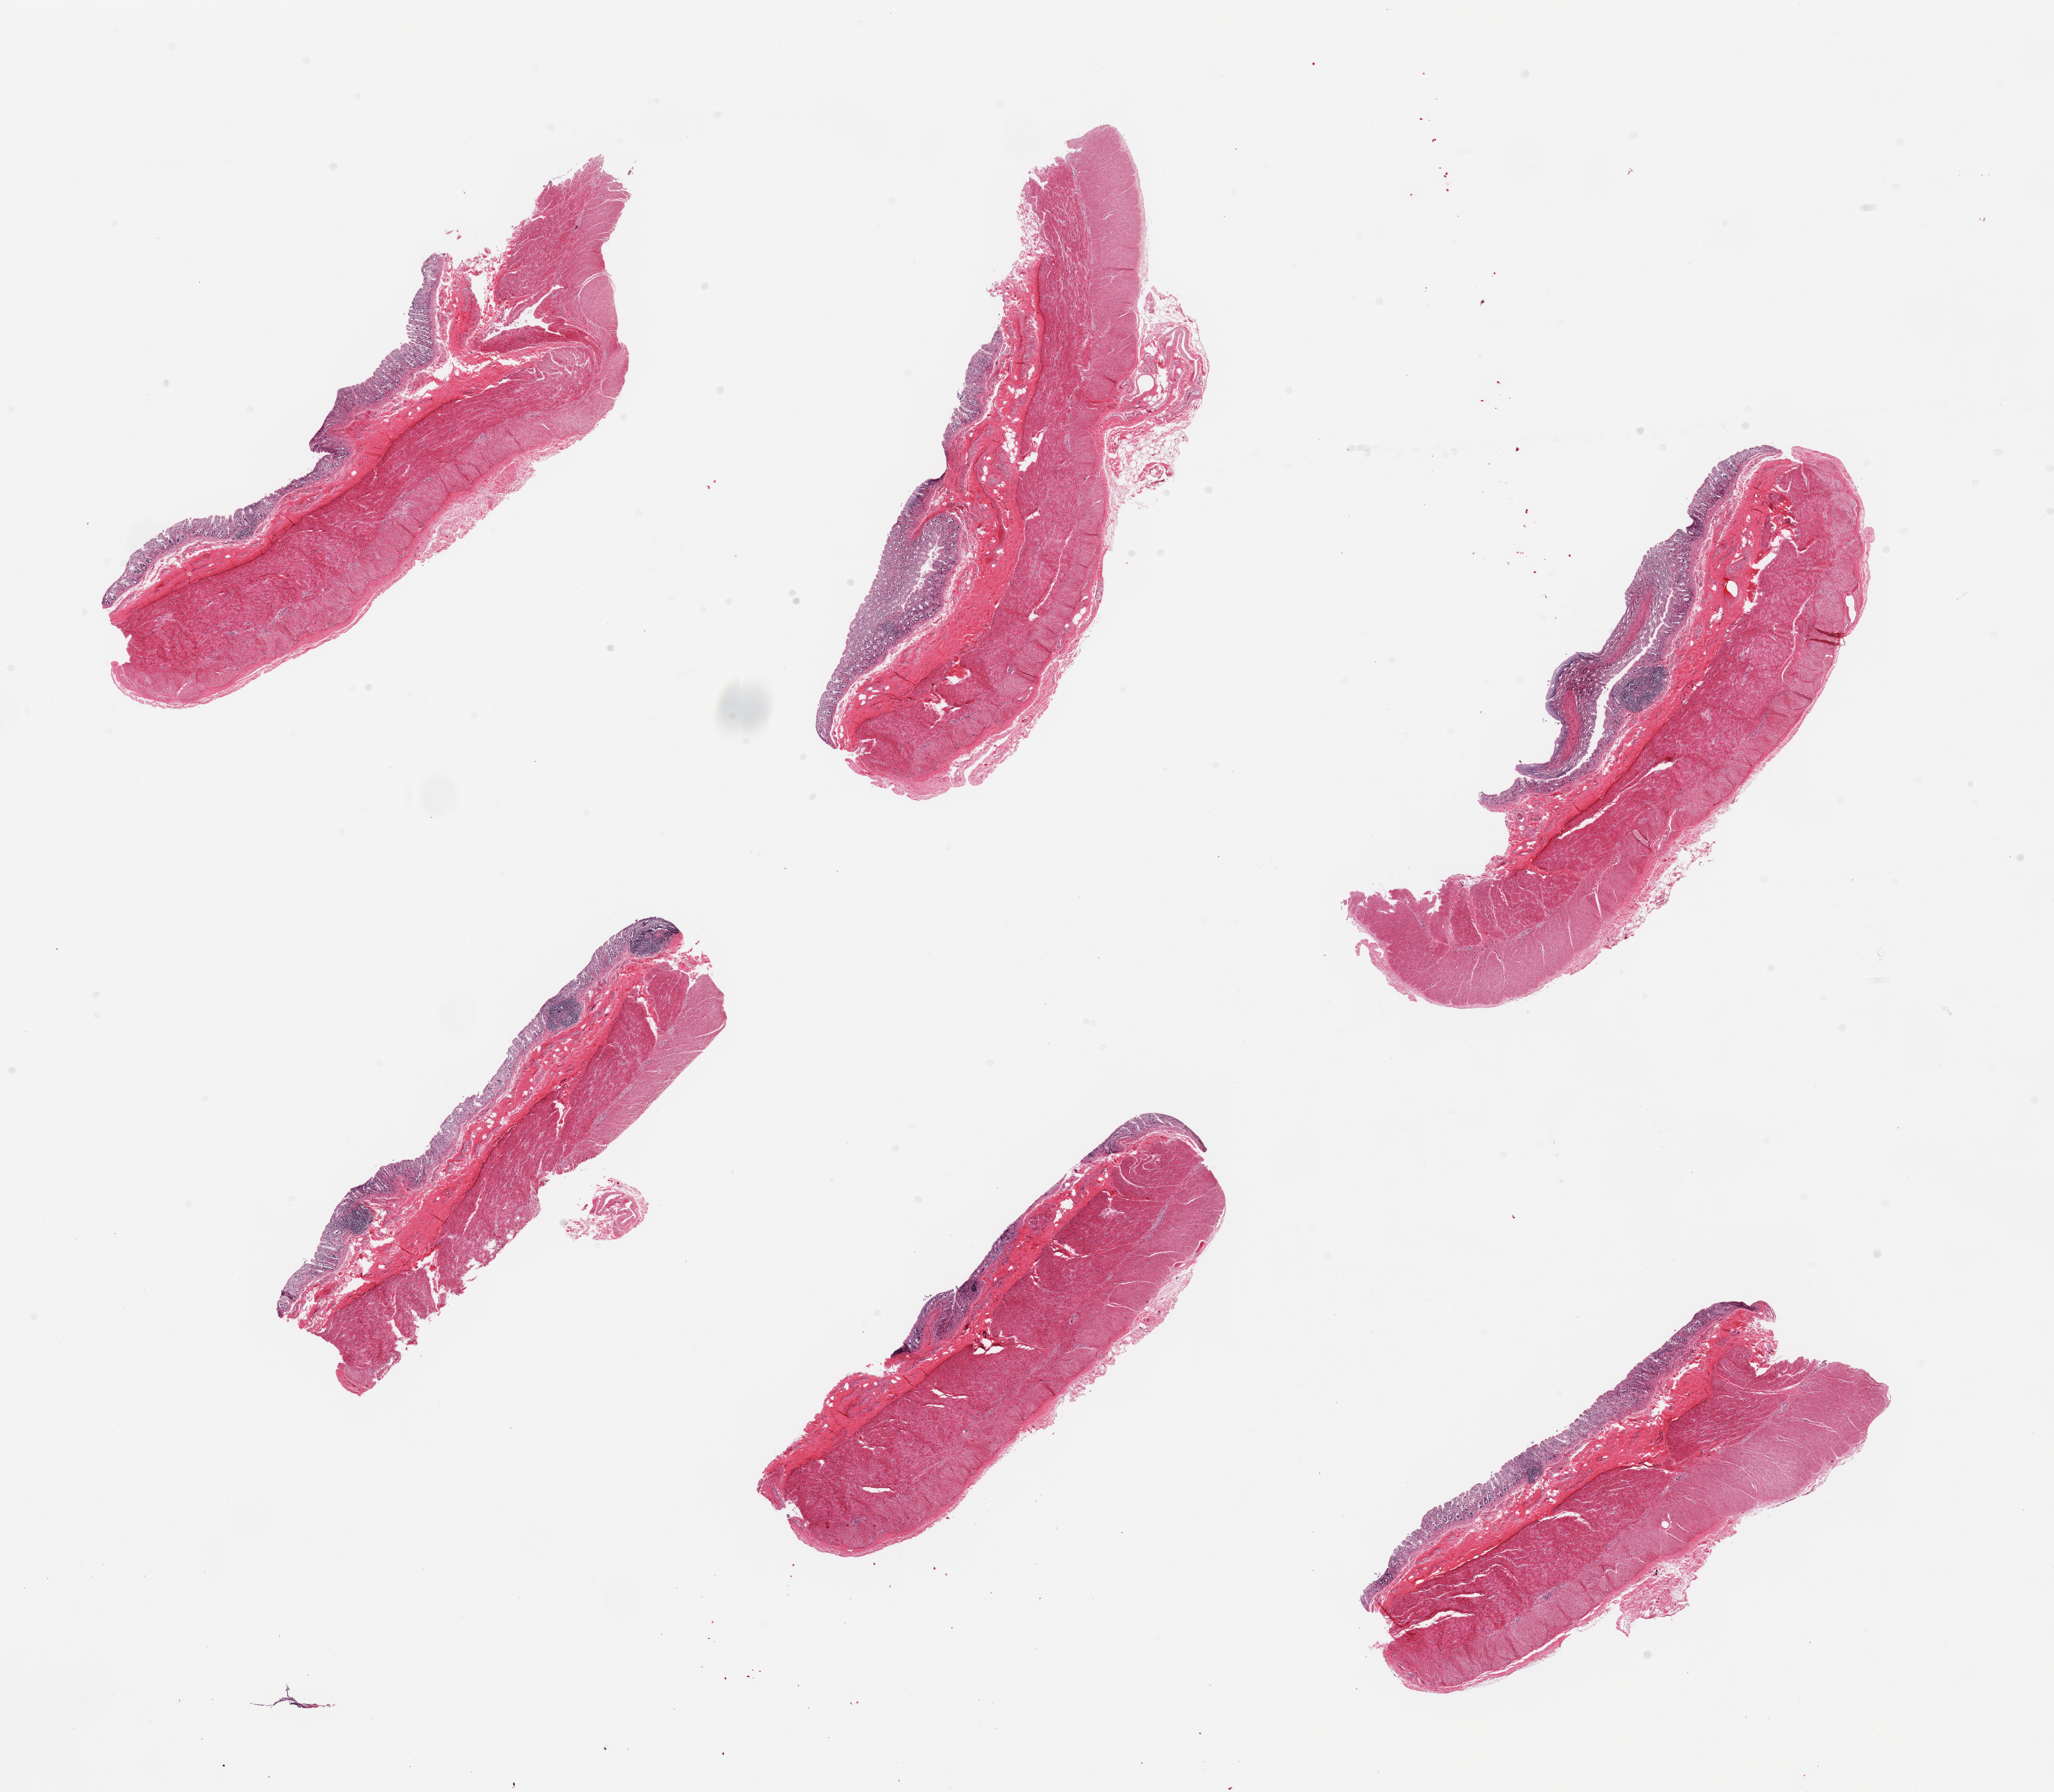
H&E whole-slide image — low-resolution overview of the scanned area, about 24.6 x 21.5 mm. PAXgene-fixed paraffin-embedded (PFPE) section. Target tissue: transverse colon. Tissue donor sample.
* pathologist's review note for this sample: 6 pieces; glands autolyzed, muscle intact; well dissected